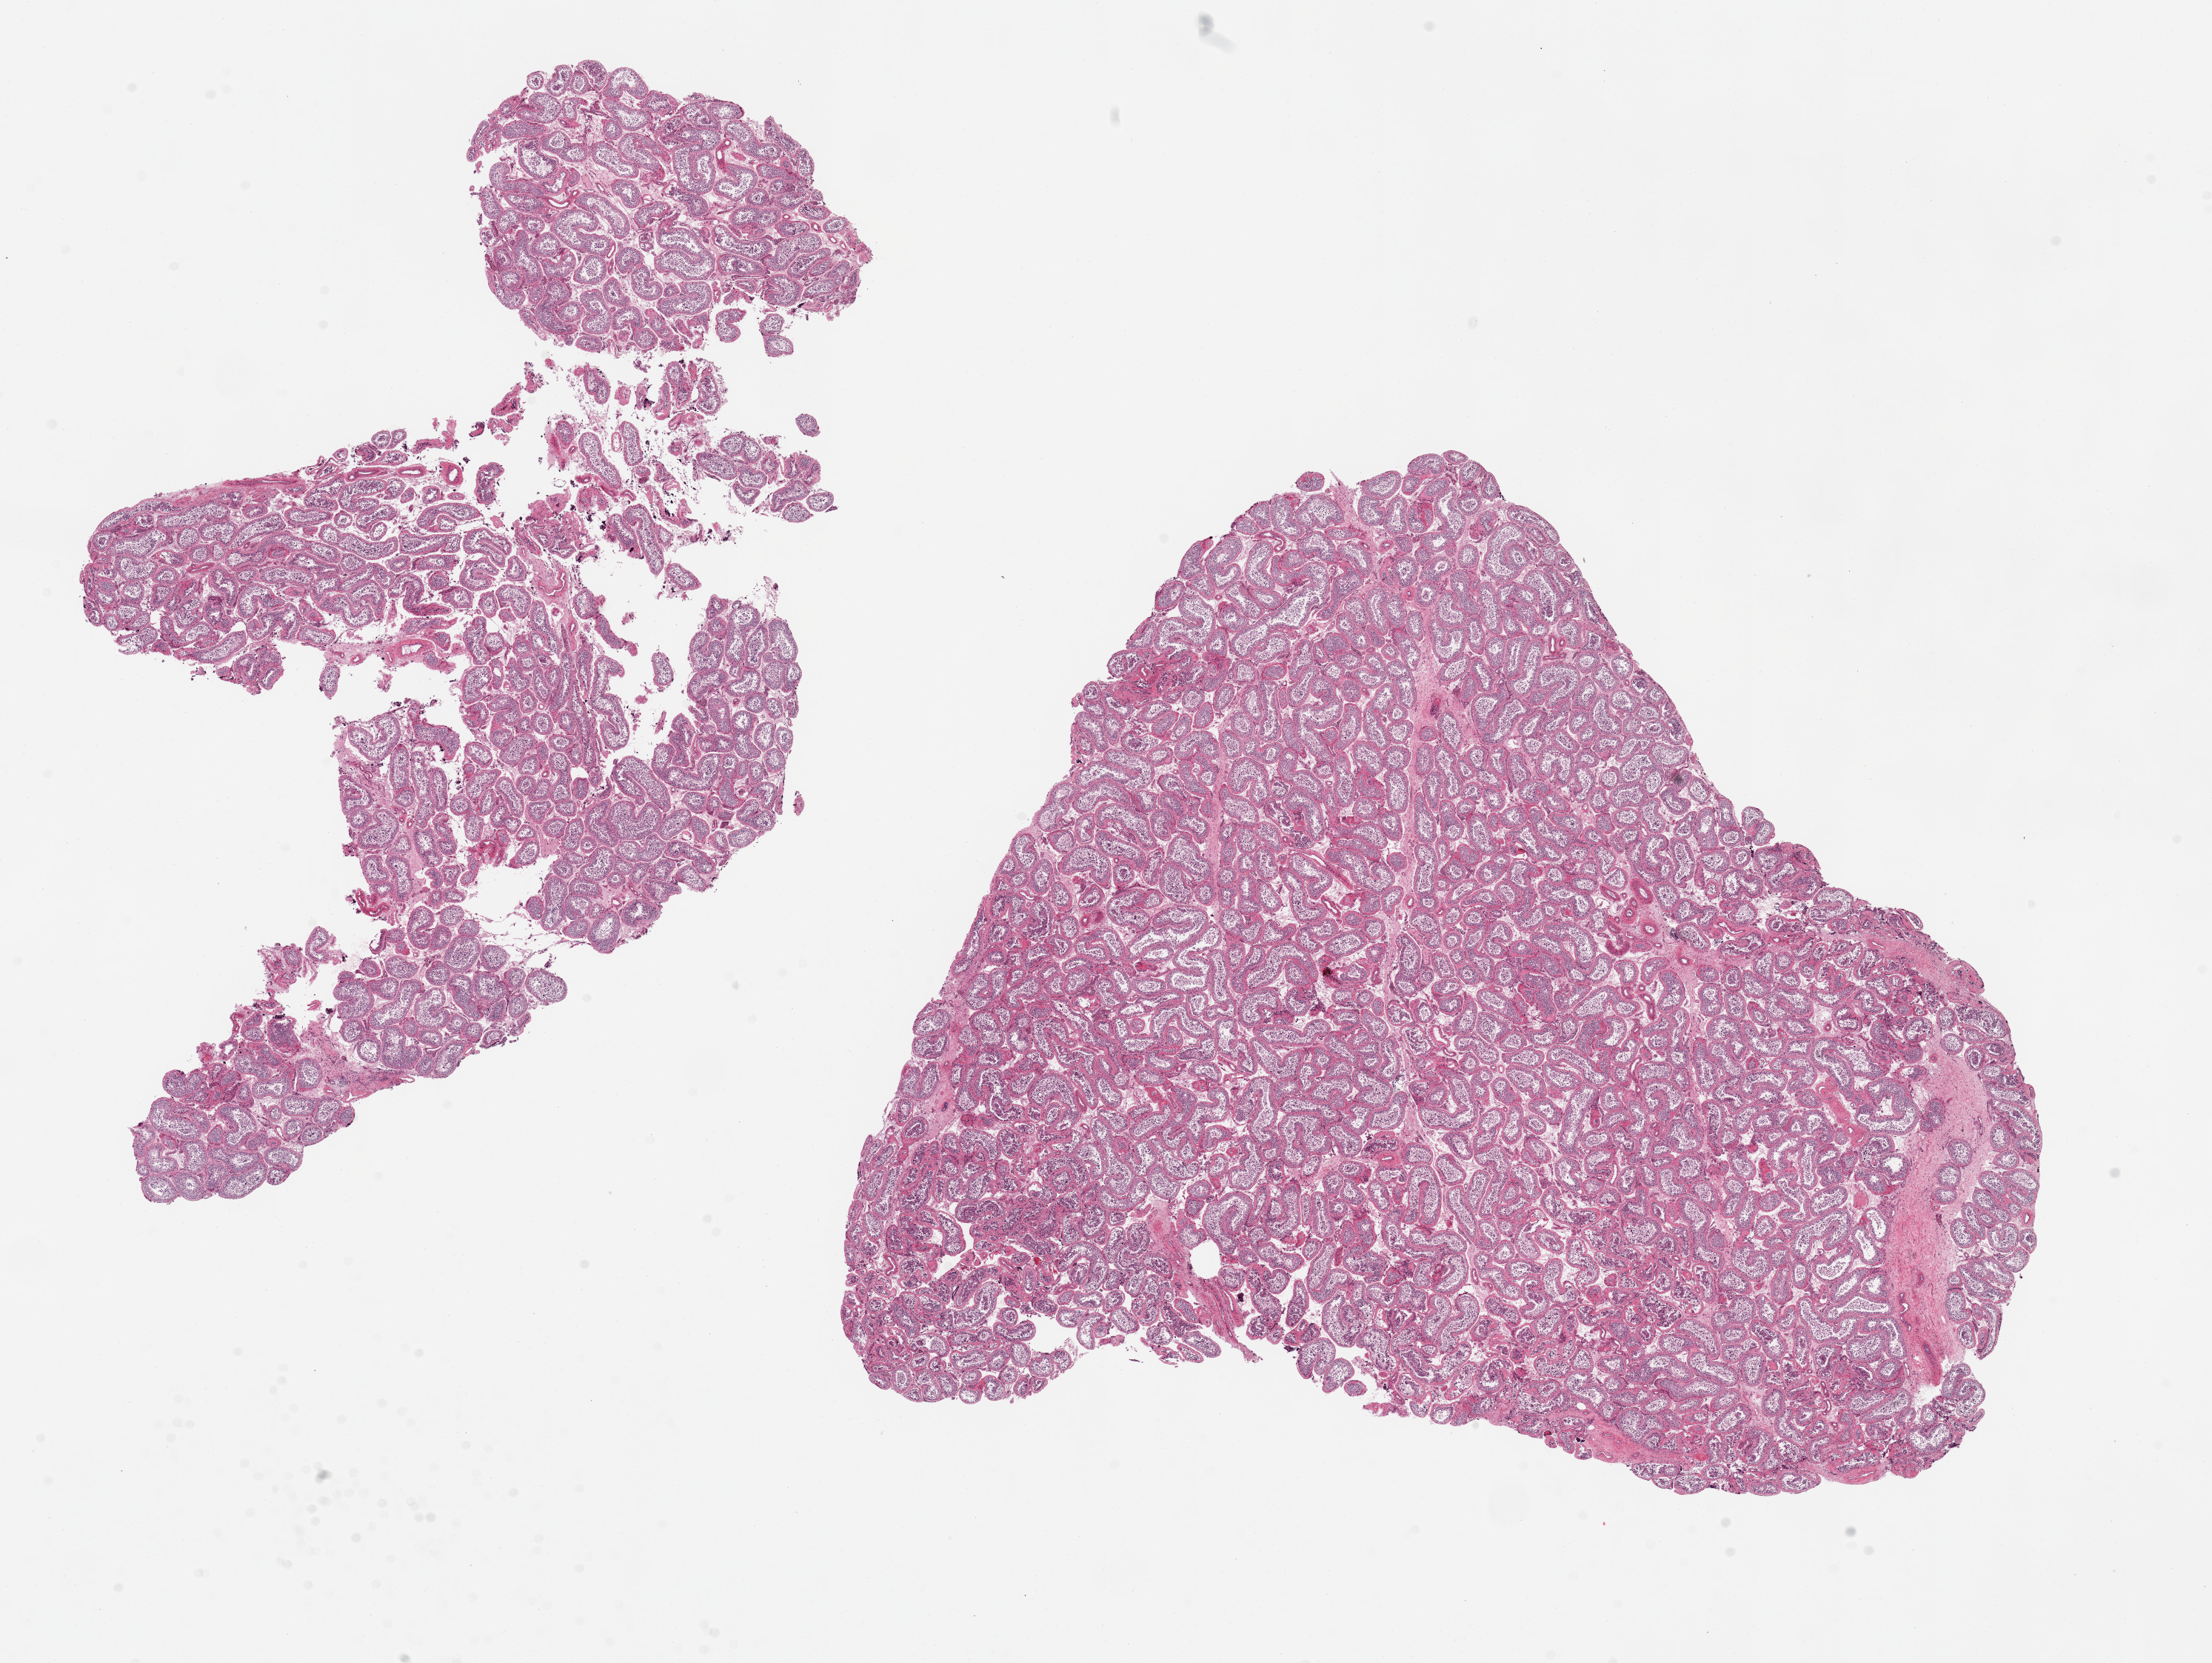
H&E whole-slide image, low-resolution overview of the scanned area, about 23.6 x 17.8 mm. PAXgene-fixed, paraffin-embedded tissue. Target tissue: testis. Tissue donor sample. Donor sex: male.
Review note (as recorded): 2 pieces, 12x11.5 and 13x7mm; spermatogenesis.